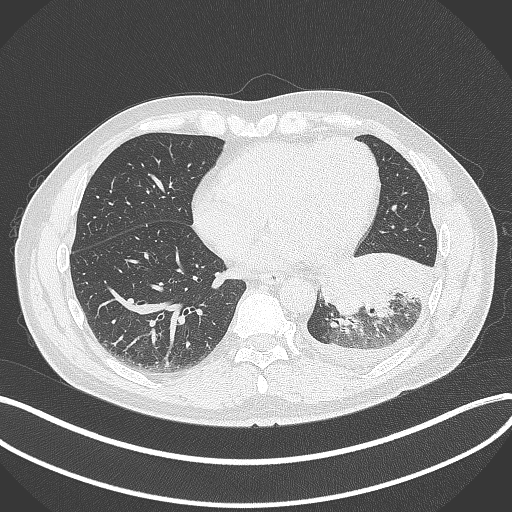
Chest CT, one axial slice; slice 122 of 342 in the series (ordered by position); reconstruction kernel B70f; 120 kVp; lung window (W 1500 / L -600 HU); 512 × 512 image matrix, field of view 400 × 400 mm. Patient: male, 58 years. Case-level facts recorded for this patient, not image findings: clinical TNM (as recorded): T3 N1 M1b.
Outlined on this slice (rectangle marked by the reading radiologist):
- lung tumour (recorded histology: small cell carcinoma): bounding box (x1, y1, x2, y2) in pixels: (320, 249, 433, 324)